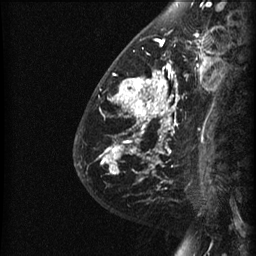
Breast MRI (dynamic contrast-enhanced), one sagittal slice; slice 17 of 60 in the series (ordered by position); dynamic contrast-enhanced series, image 2 of 3 at this slice position (ordered by acquisition); 1.5 T; TE 4.2 ms, TR 22.7 ms; 1.5 mm slice thickness; 256 × 256 image matrix, field of view 180 × 180 mm. Female patient, age 48 years. Case-level facts recorded for this patient, not image findings: setting: breast cancer imaged before/during neoadjuvant chemotherapy; receptor status: triple-negative.
Outlined on this slice (semi-automatically segmented with operator editing):
- analysis volume of interest (the breast-tissue region the enhancement analysis was run in; not a lesion): box from (x=89, y=27) to (x=191, y=180) px
- tumour enhancement mask (voxels above the 90 % enhancement threshold inside the analysis volume of interest): (x=98, y=33)–(x=191, y=180)